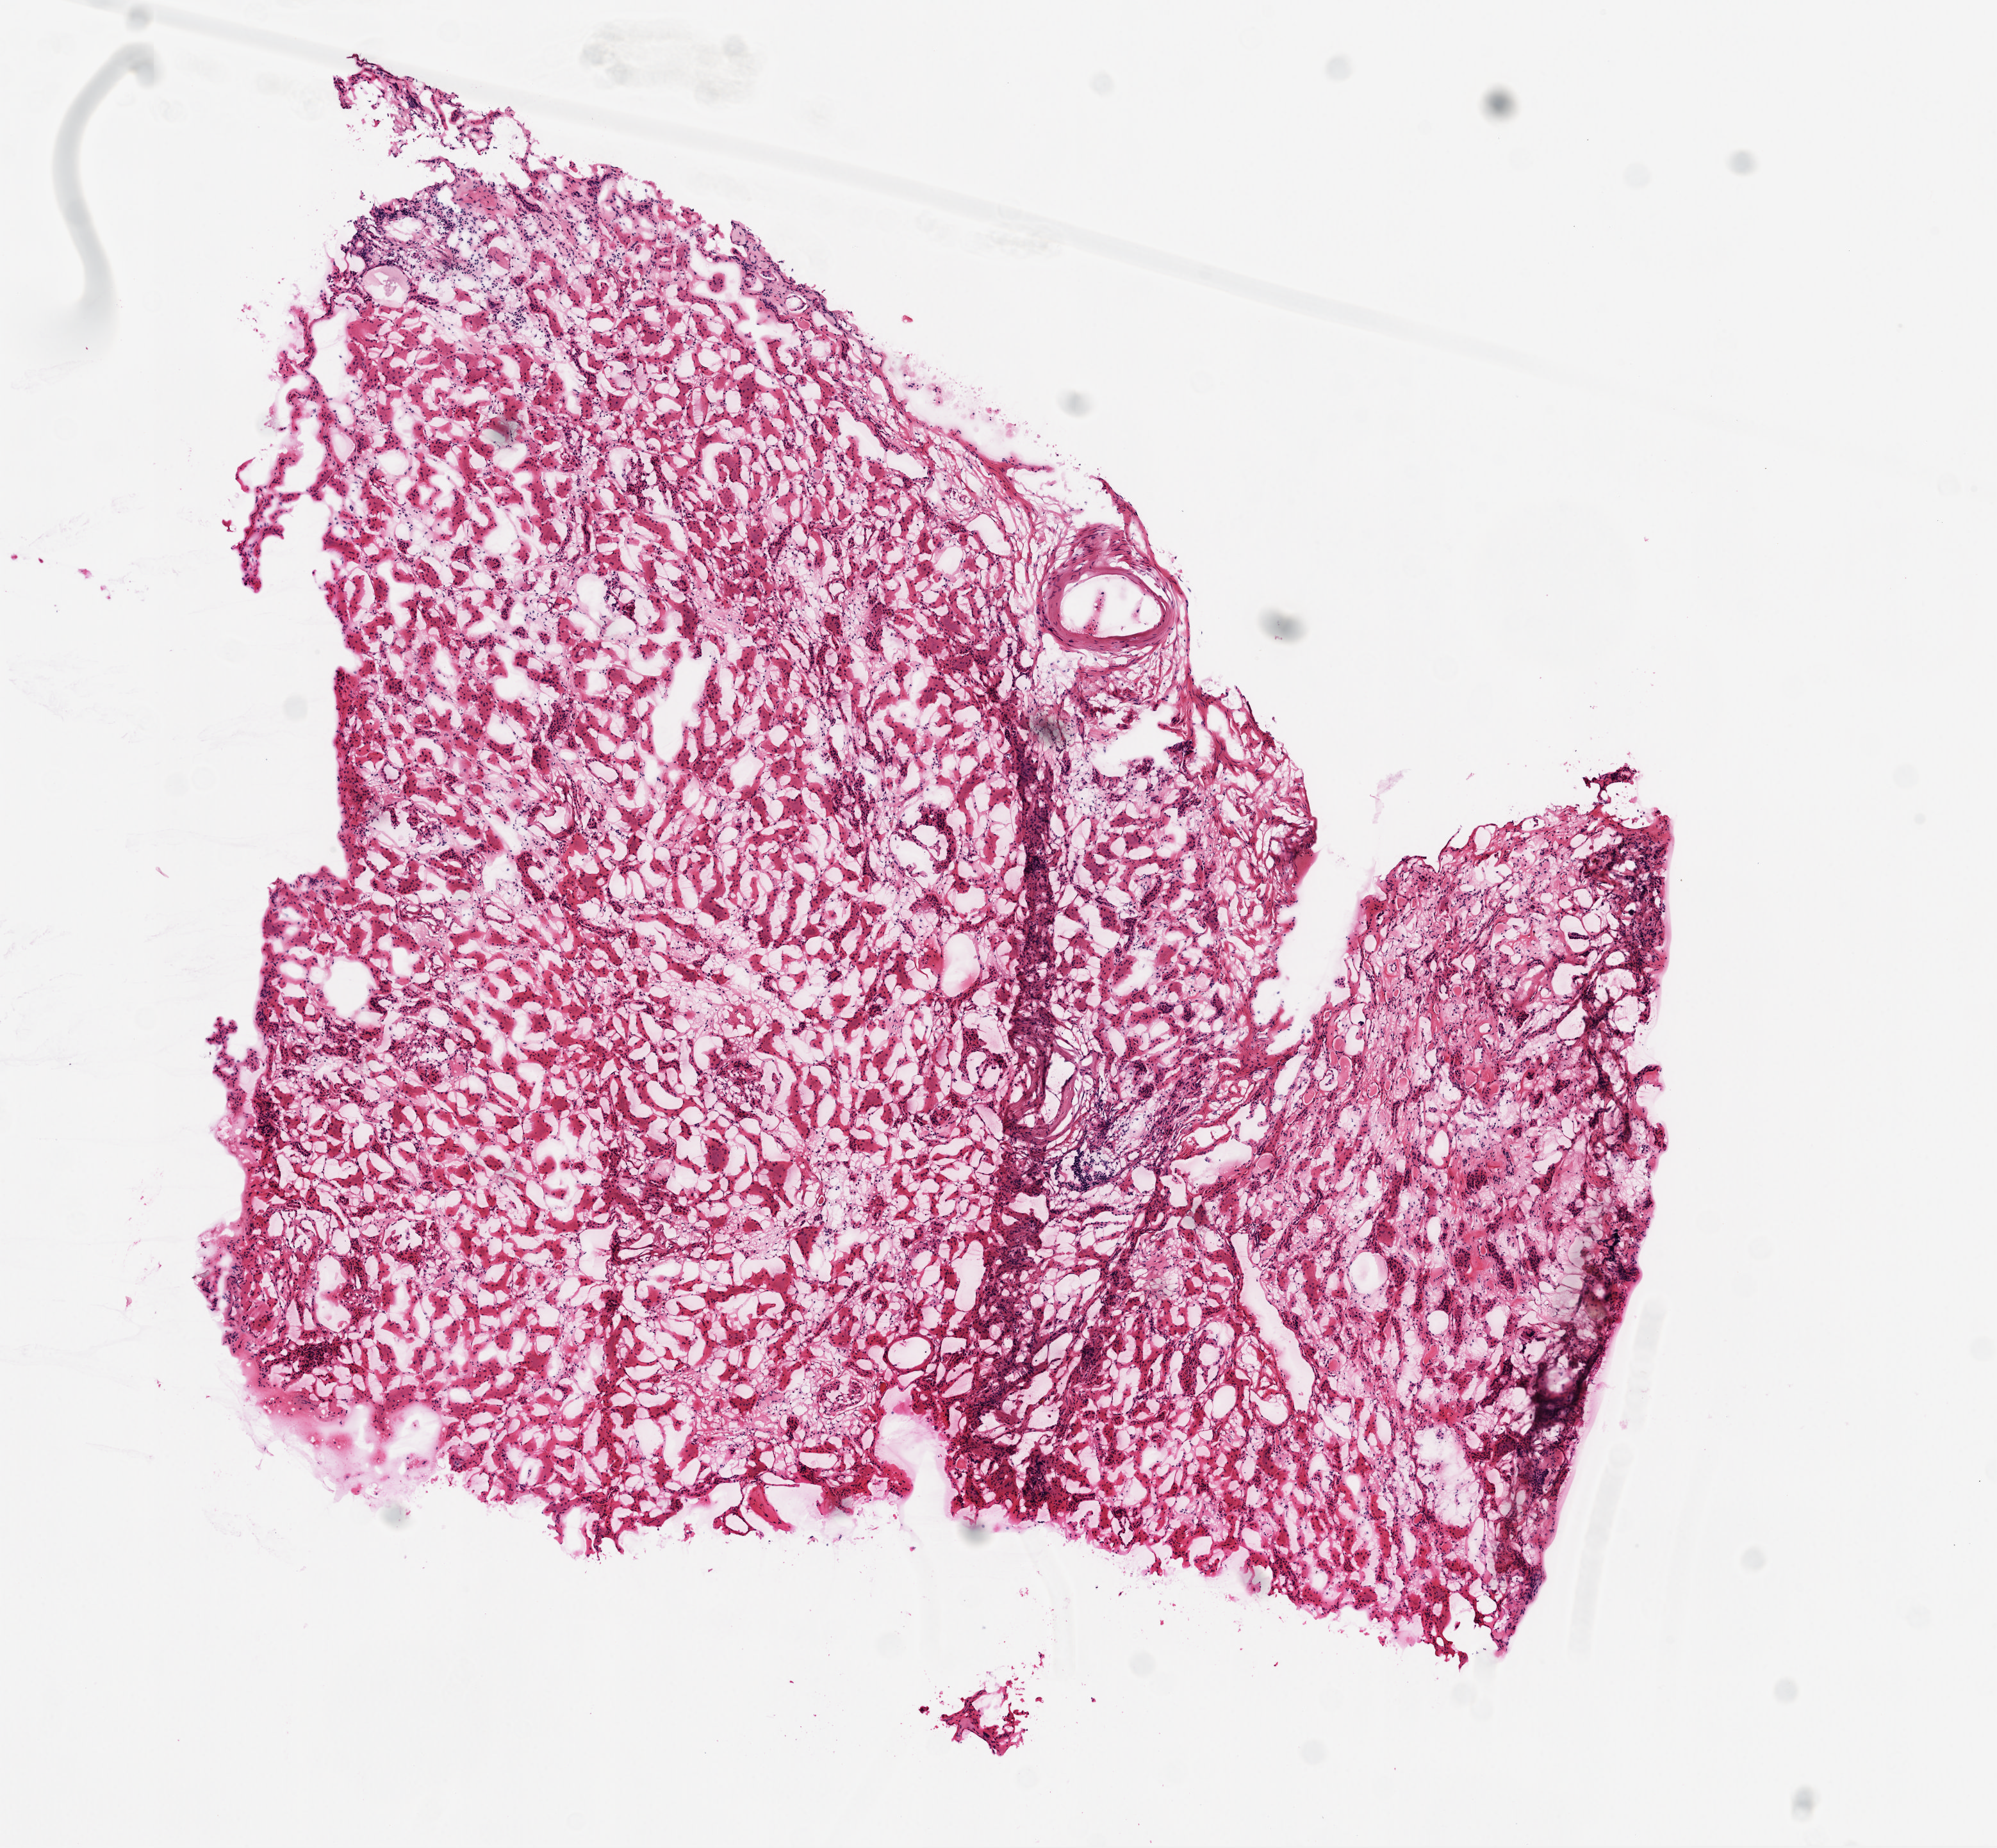
Digitized H&E-stained tissue section (whole slide) — low-resolution overview of the scanned area, about 6.3 x 5.8 mm; frozen section from the top of the tissue portion; sample: solid tissue normal (non-tumour tissue), kidney. Male patient; age at initial diagnosis 78 years.
This section: solid tissue normal (non-tumour) sample from the same patient. Patient diagnosis: Clear cell adenocarcinoma, NOS.